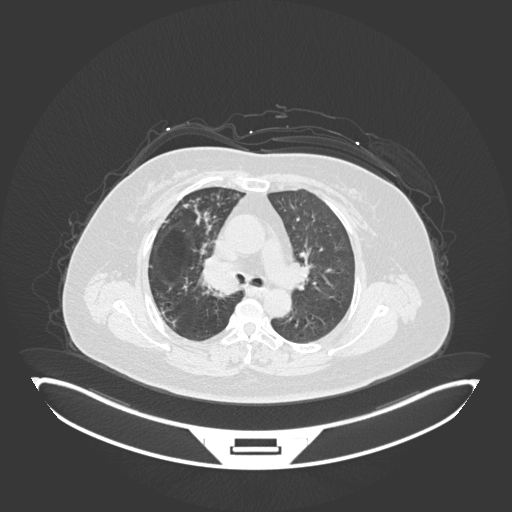
Chest CT, one axial slice. Slice 113 of 245 in the series (ordered by position). 120 kVp. Lung window (W 1500 / L -600 HU). 1 mm slice thickness. 512 × 512 image matrix, field of view 500 × 500 mm. Female patient, age 60 years. From the clinical record (not read from this slice): clinical TNM (as recorded): T1c N0 M0.
Outlined on this slice (rectangle marked by the reading radiologist):
- lung tumour (recorded histology: squamous cell carcinoma): bounding box [x1, y1, x2, y2] px = [198, 254, 244, 299]